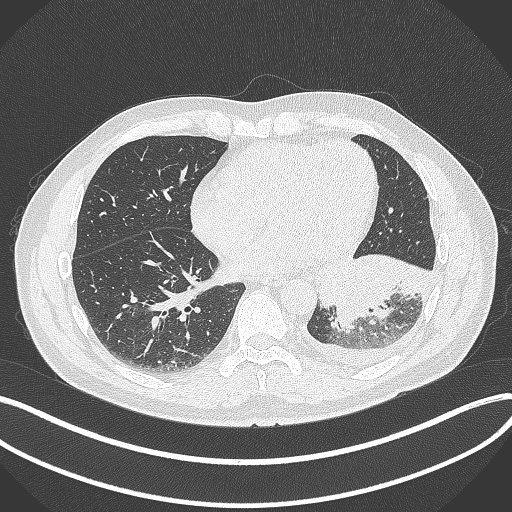
Chest CT, one axial slice. Slice 128 of 342 in the series (ordered by position). 120 kVp. Lung window (W 1500 / L -600 HU). 512 × 512 image matrix, field of view 400 × 400 mm. Male patient, age 58 years. Case-level facts recorded for this patient, not image findings: clinical TNM (as recorded): T3 N1 M1b.
Annotated regions visible in this slice (bounding box drawn by a radiologist):
- lung tumour (recorded histology: small cell carcinoma): bounding box <312,251,434,335> (left, top, right, bottom; pixels)